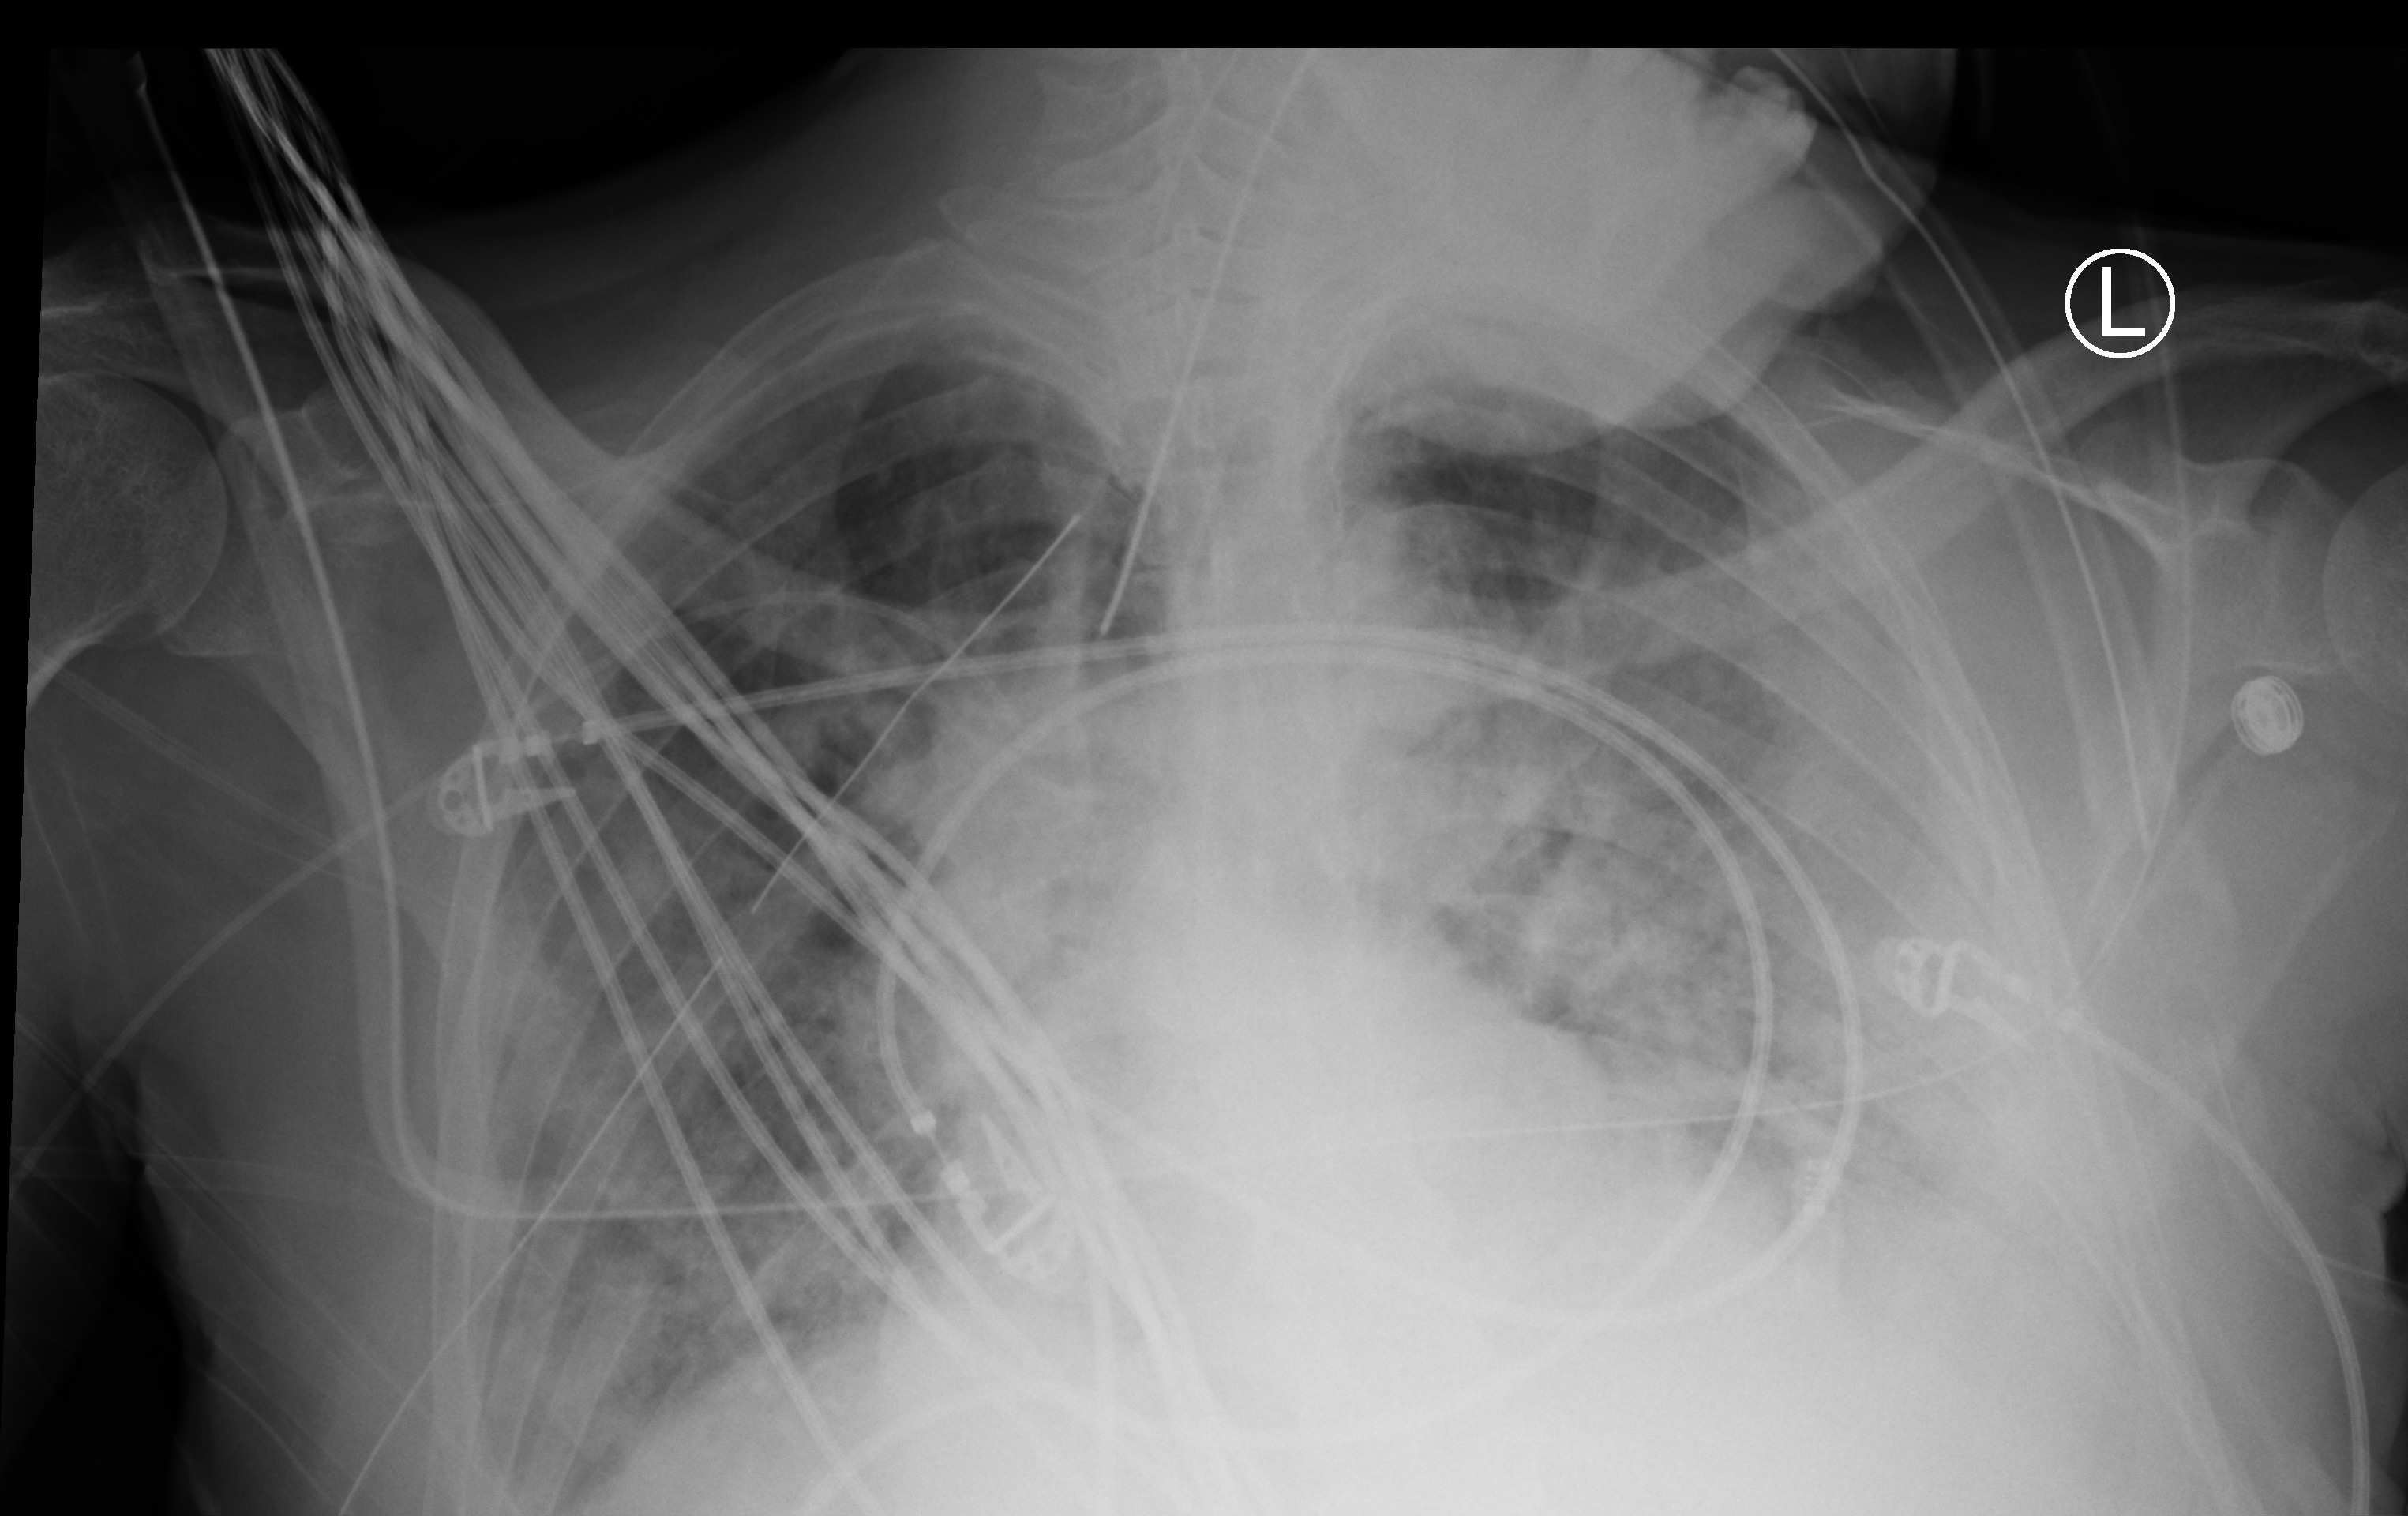
Bedside chest radiograph (computed radiography). Patient hospitalised with COVID-19; male, aged 18–59 years.
Hospital-stay facts (about this admission, not read from this image; timing relative to this image not recorded):
- hypertension (admission record): no